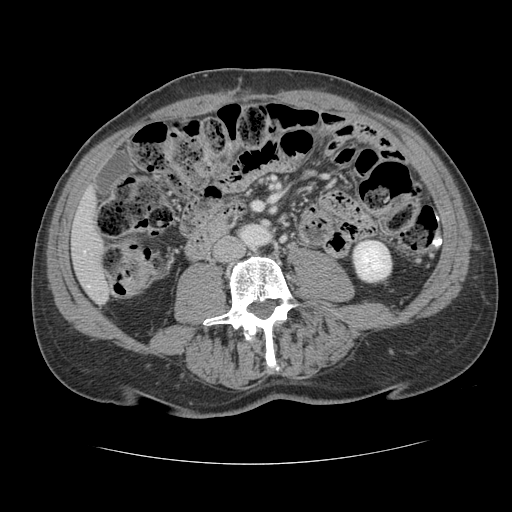
Contrast-enhanced abdominal CT, one axial slice. Slice 27 of 134 in the series (ordered by position). Reconstruction kernel STANDARD. Intravenous contrast given. Soft-tissue window (W 400 / L 40 HU). 2.5 mm slice thickness. 512 × 512 image matrix. Male patient, age 68 years. From the clinical record (not read from this slice): diagnosis: colorectal cancer liver metastases, imaged before liver resection; multiple liver metastases: yes; largest metastasis: 2.2 cm.
Outlined on this slice (expert manual segmentation):
- liver: box from (x=72, y=192) to (x=110, y=302) px
- planned liver remnant (the part of the liver to remain after resection): (x=72, y=193)–(x=110, y=302)